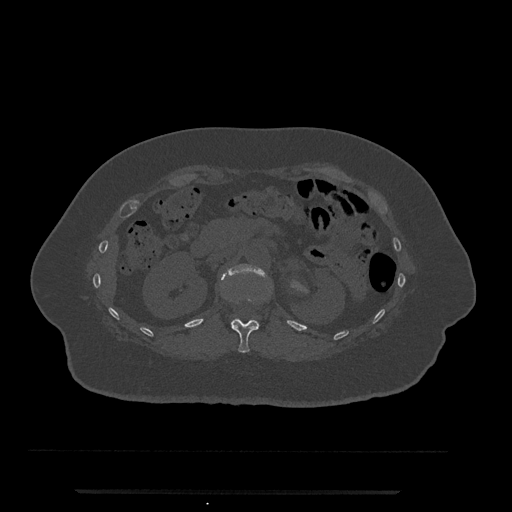
CT including the spine, one axial slice; position 144 of 797 along the scan axis; bone window (W 1800 / L 400 HU); 512 × 512 image matrix. Patient: female, 51 years. From the clinical record (not read from this slice): primary cancer: neuro; vertebrae with lytic lesions (as recorded): T8.
Outlined on this slice (semi-automatically segmented with operator editing):
- L1 vertebra: bounding box <222,264,265,322> (left, top, right, bottom; pixels)
- T12 vertebra: <231,300,259,353>